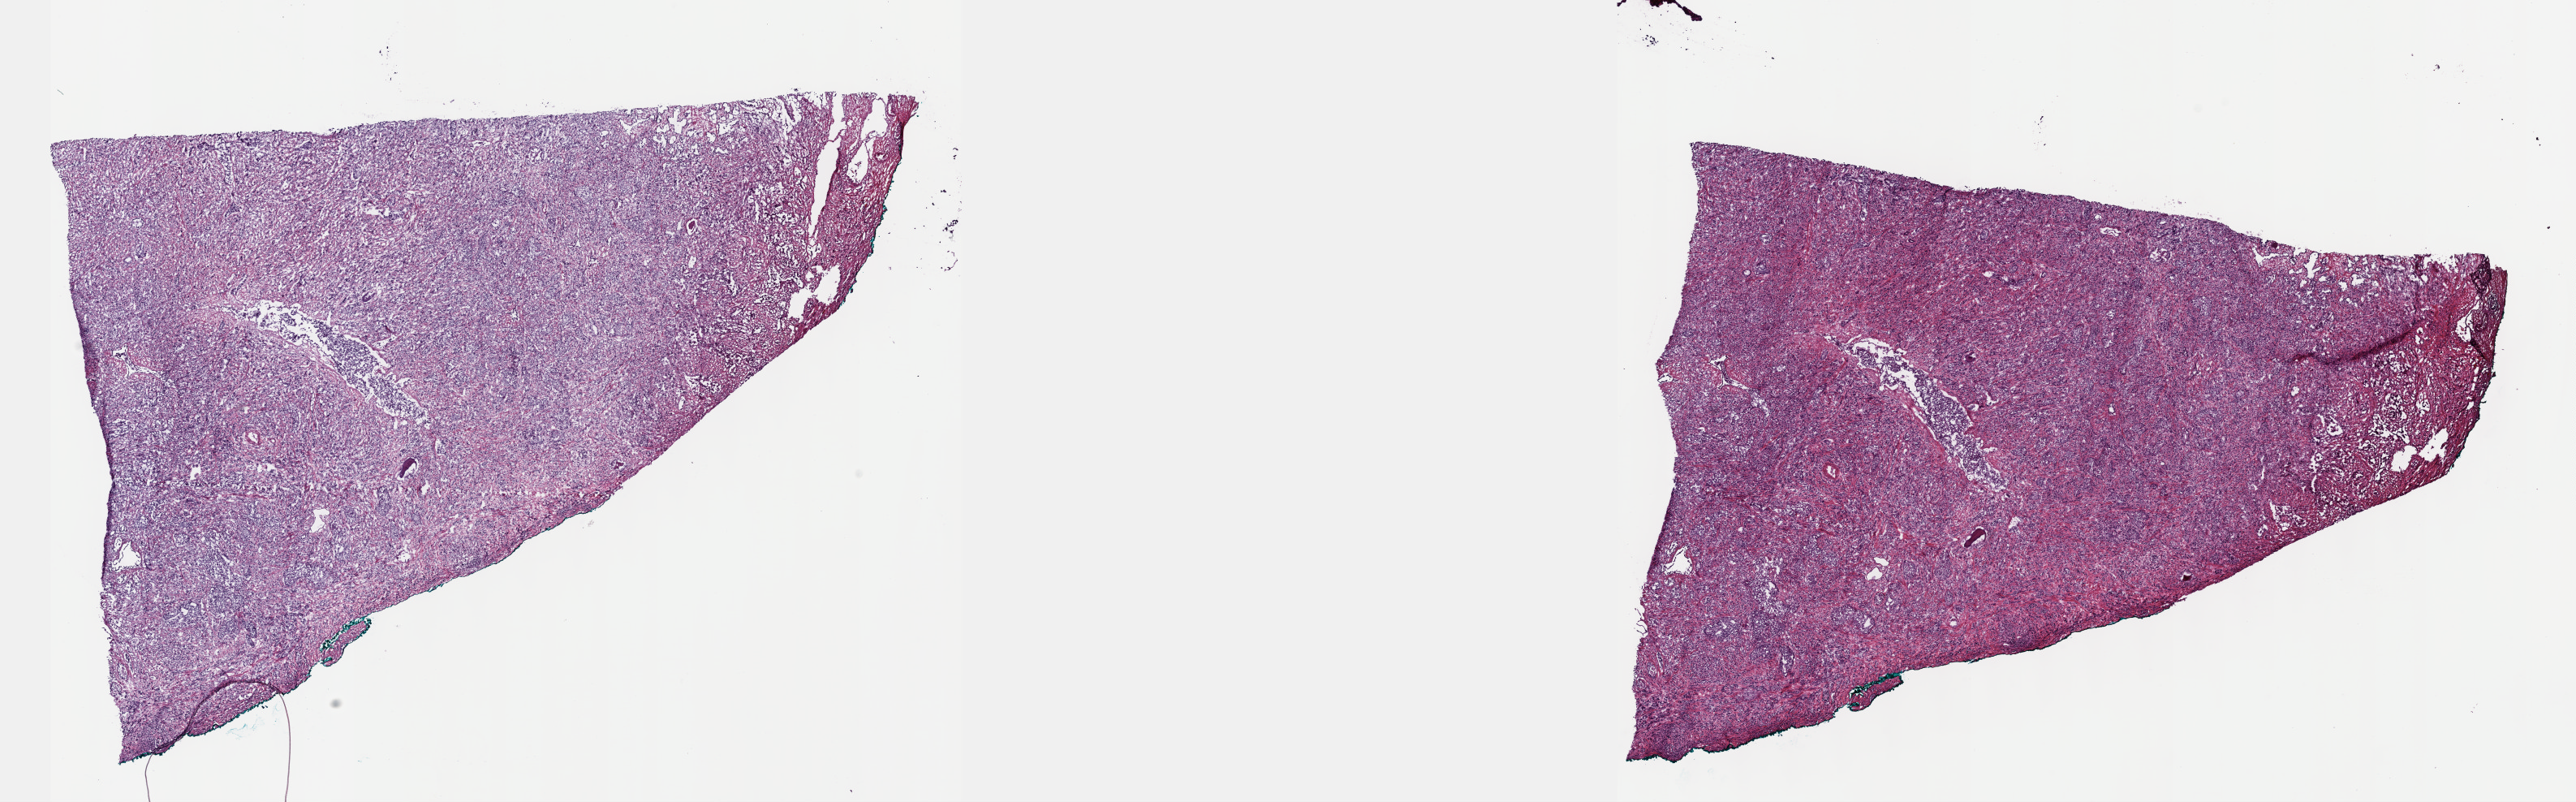
Digitized H&E-stained tissue section (whole slide) — whole scanned area (about 25.7 x 8.0 mm) shown as a low-resolution overview; frozen section from the top of the tissue portion; primary tumour sample from the prostate. Male, age 72 years at initial diagnosis. Gleason score: 9 (4+5). Composition of this section per pathologist review: tumour cells 70%, tumour nuclei 70%, normal cells 0%, stromal cells 30%, necrosis 0%. Infiltration values recorded for this section: lymphocyte infiltration 0%, monocyte infiltration 0%, neutrophil infiltration 0%.
Diagnosis: Adenocarcinoma, NOS (prostate gland). Lymph nodes positive (case pathology): 2 of 11 examined.